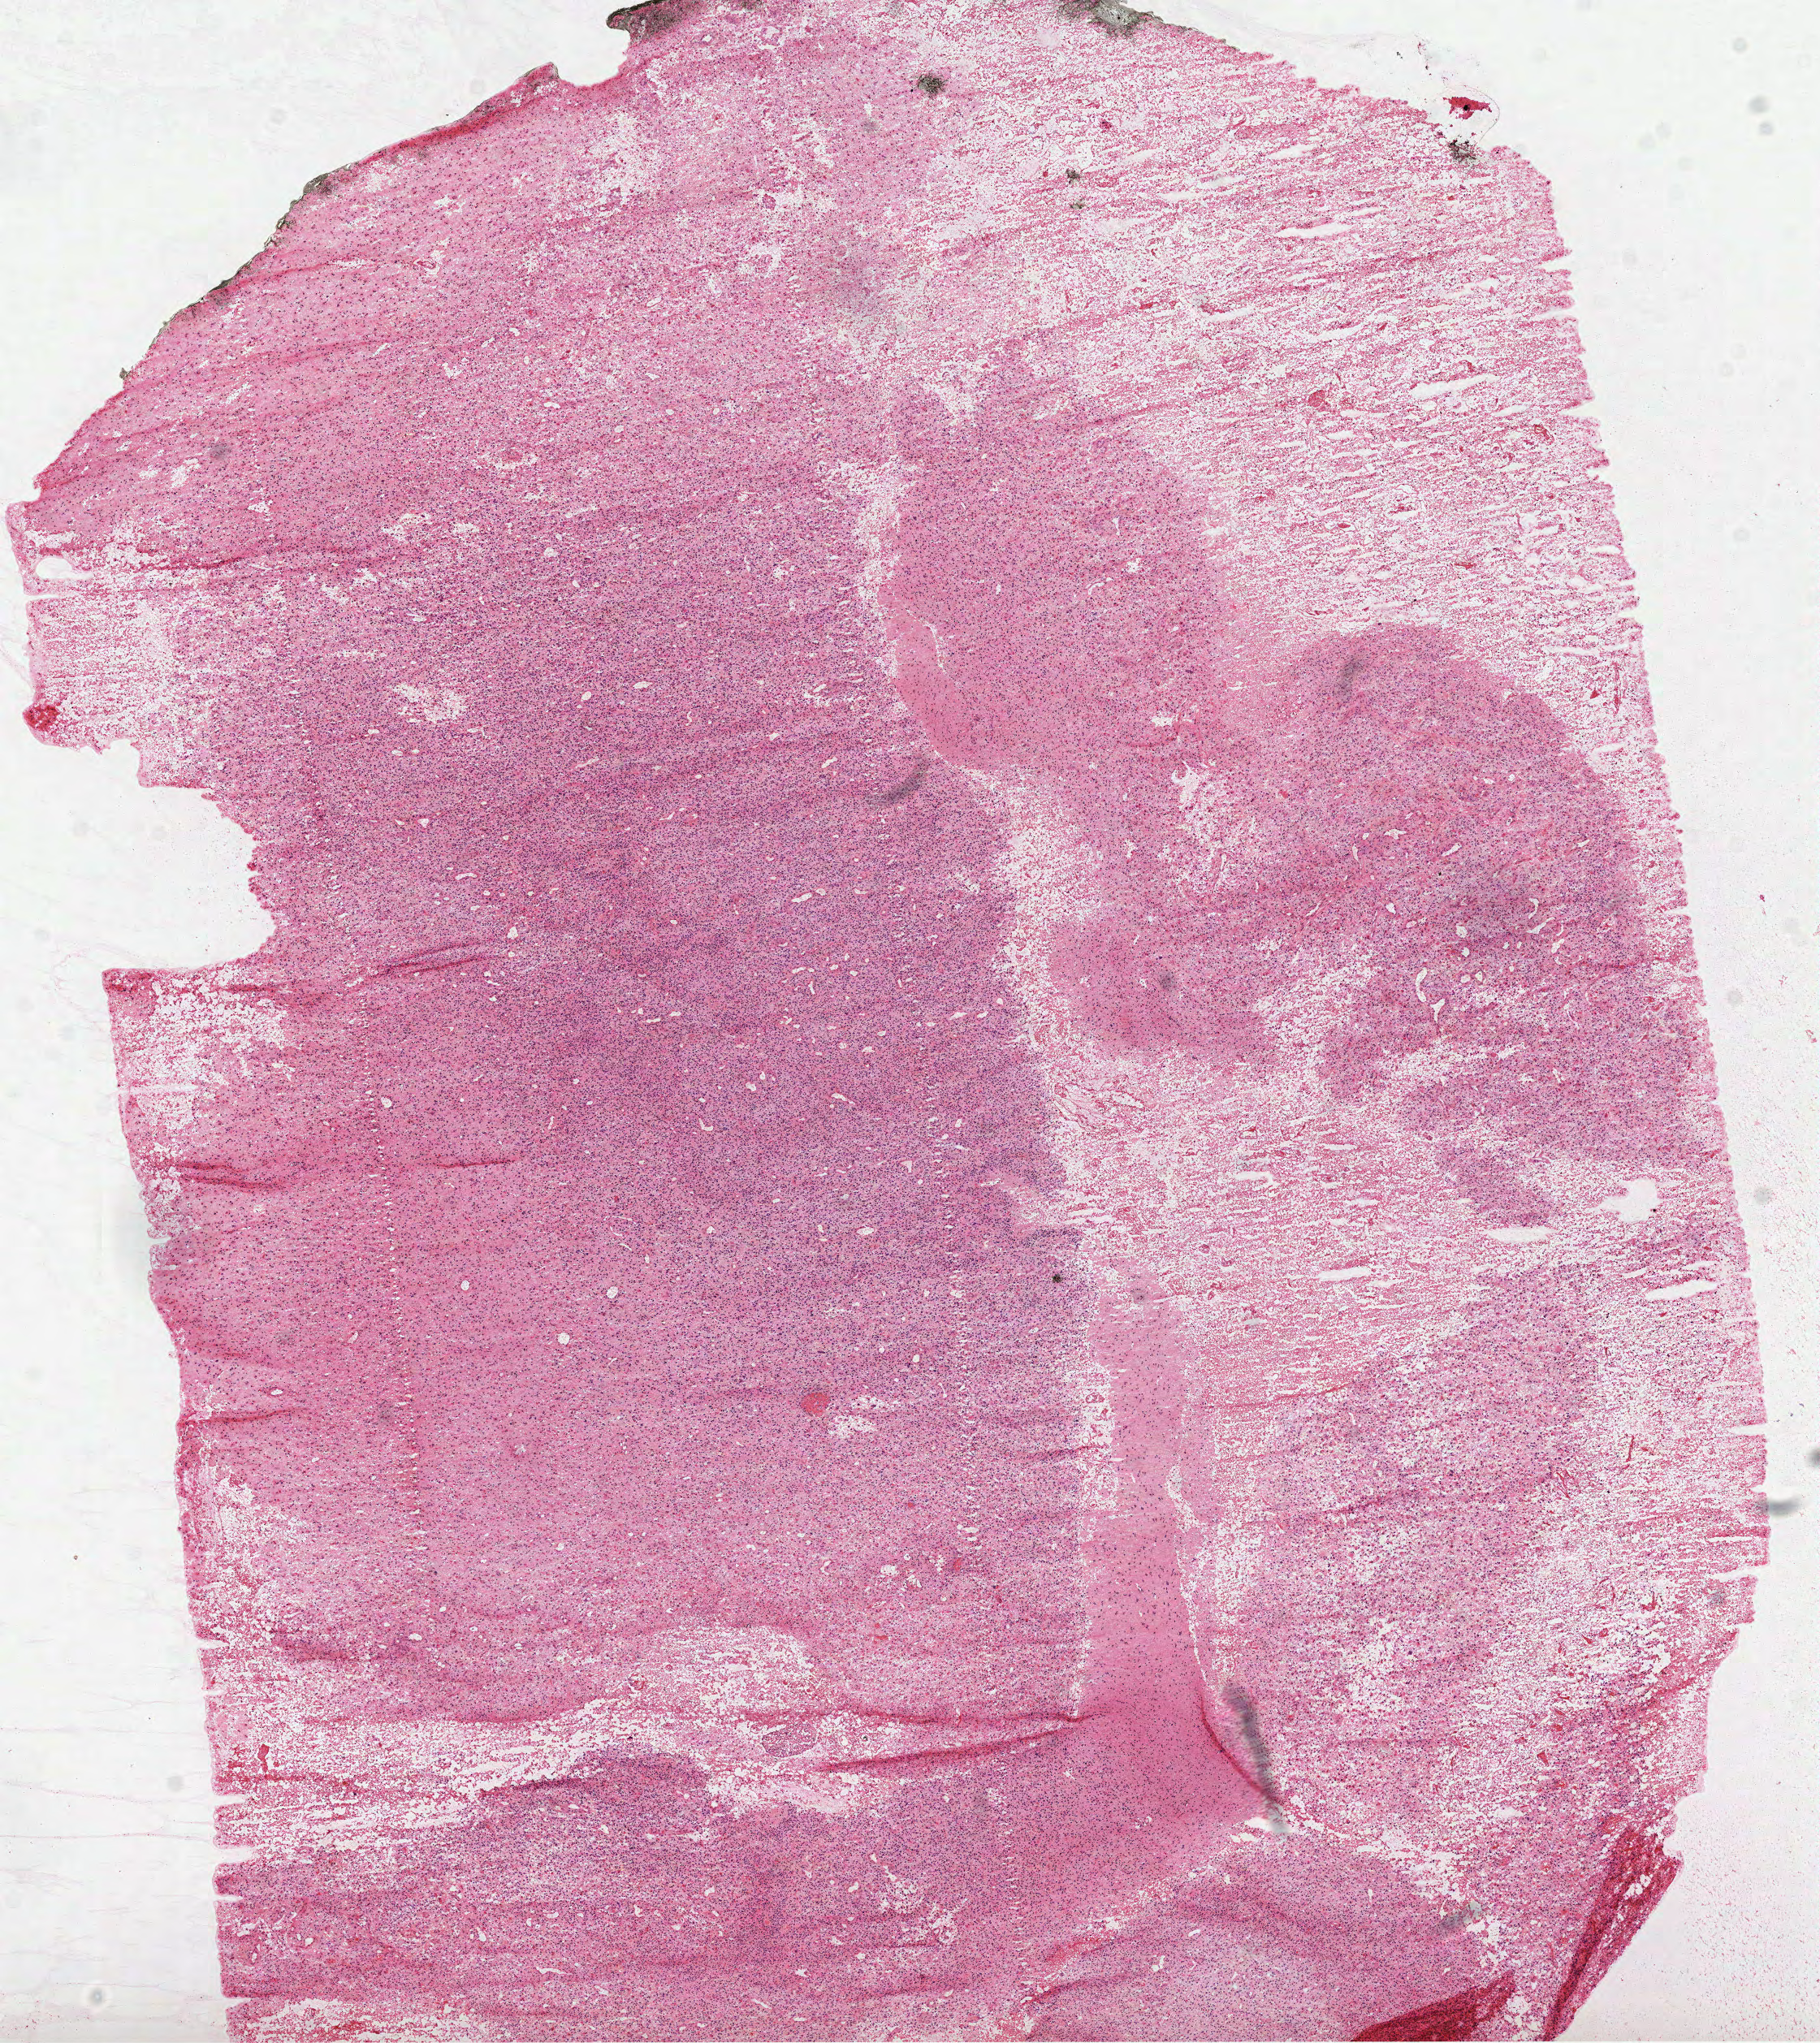
H&E-stained whole-slide image — shown as a low-resolution overview of the whole scanned area (about 9.0 x 10.1 mm). Frozen section from the top of the tissue portion. Brain, primary tumour sample. Patient: male, age at initial diagnosis 67 years. Composition of this section per pathologist review: tumour cells 60%, tumour nuclei 80%, normal cells 0%, stromal cells 0%, necrosis 40%.
• histologic diagnosis: Glioblastoma